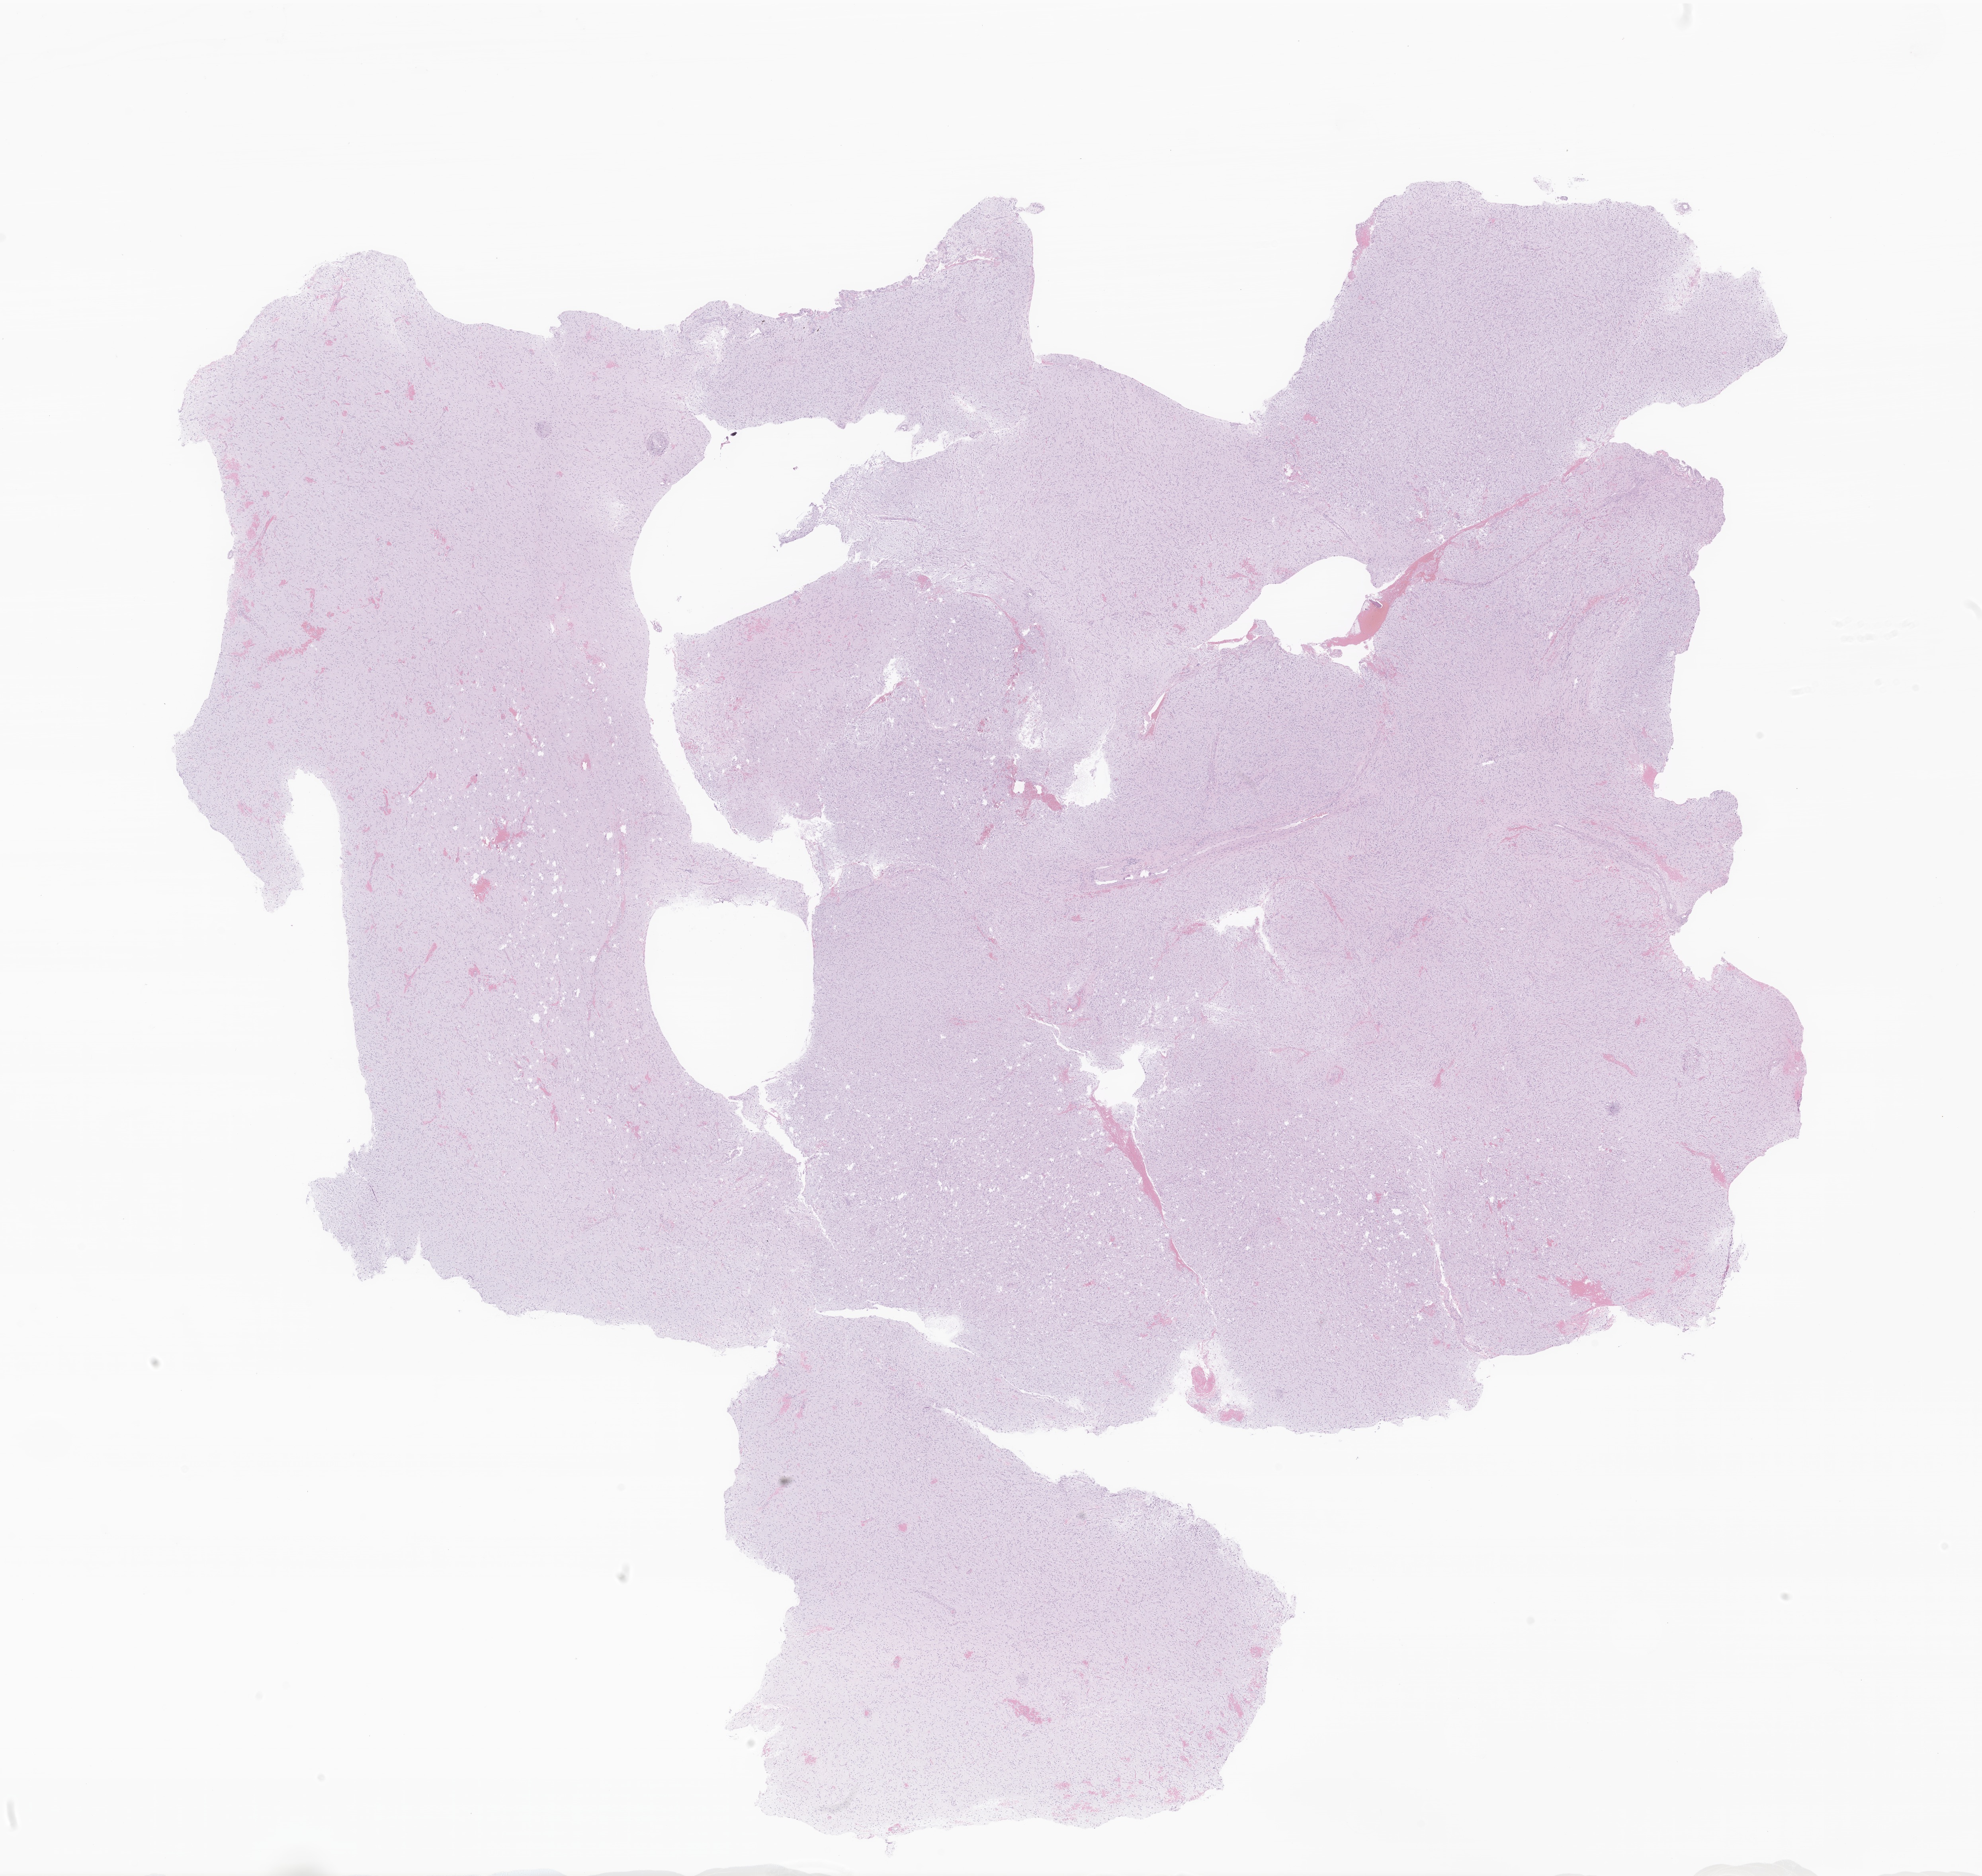
Digitized hematoxylin and eosin (H&E)-stained section of tumor tissue from the frontal lobe, low-resolution overview of the scanned area, about 21.0 x 19.9 mm, formalin-fixed, paraffin-embedded (FFPE) tissue. Female patient, age 140 months (11 years 8 months).
Diagnosis (ICD-O-3 morphology term): Glioma, malignant.